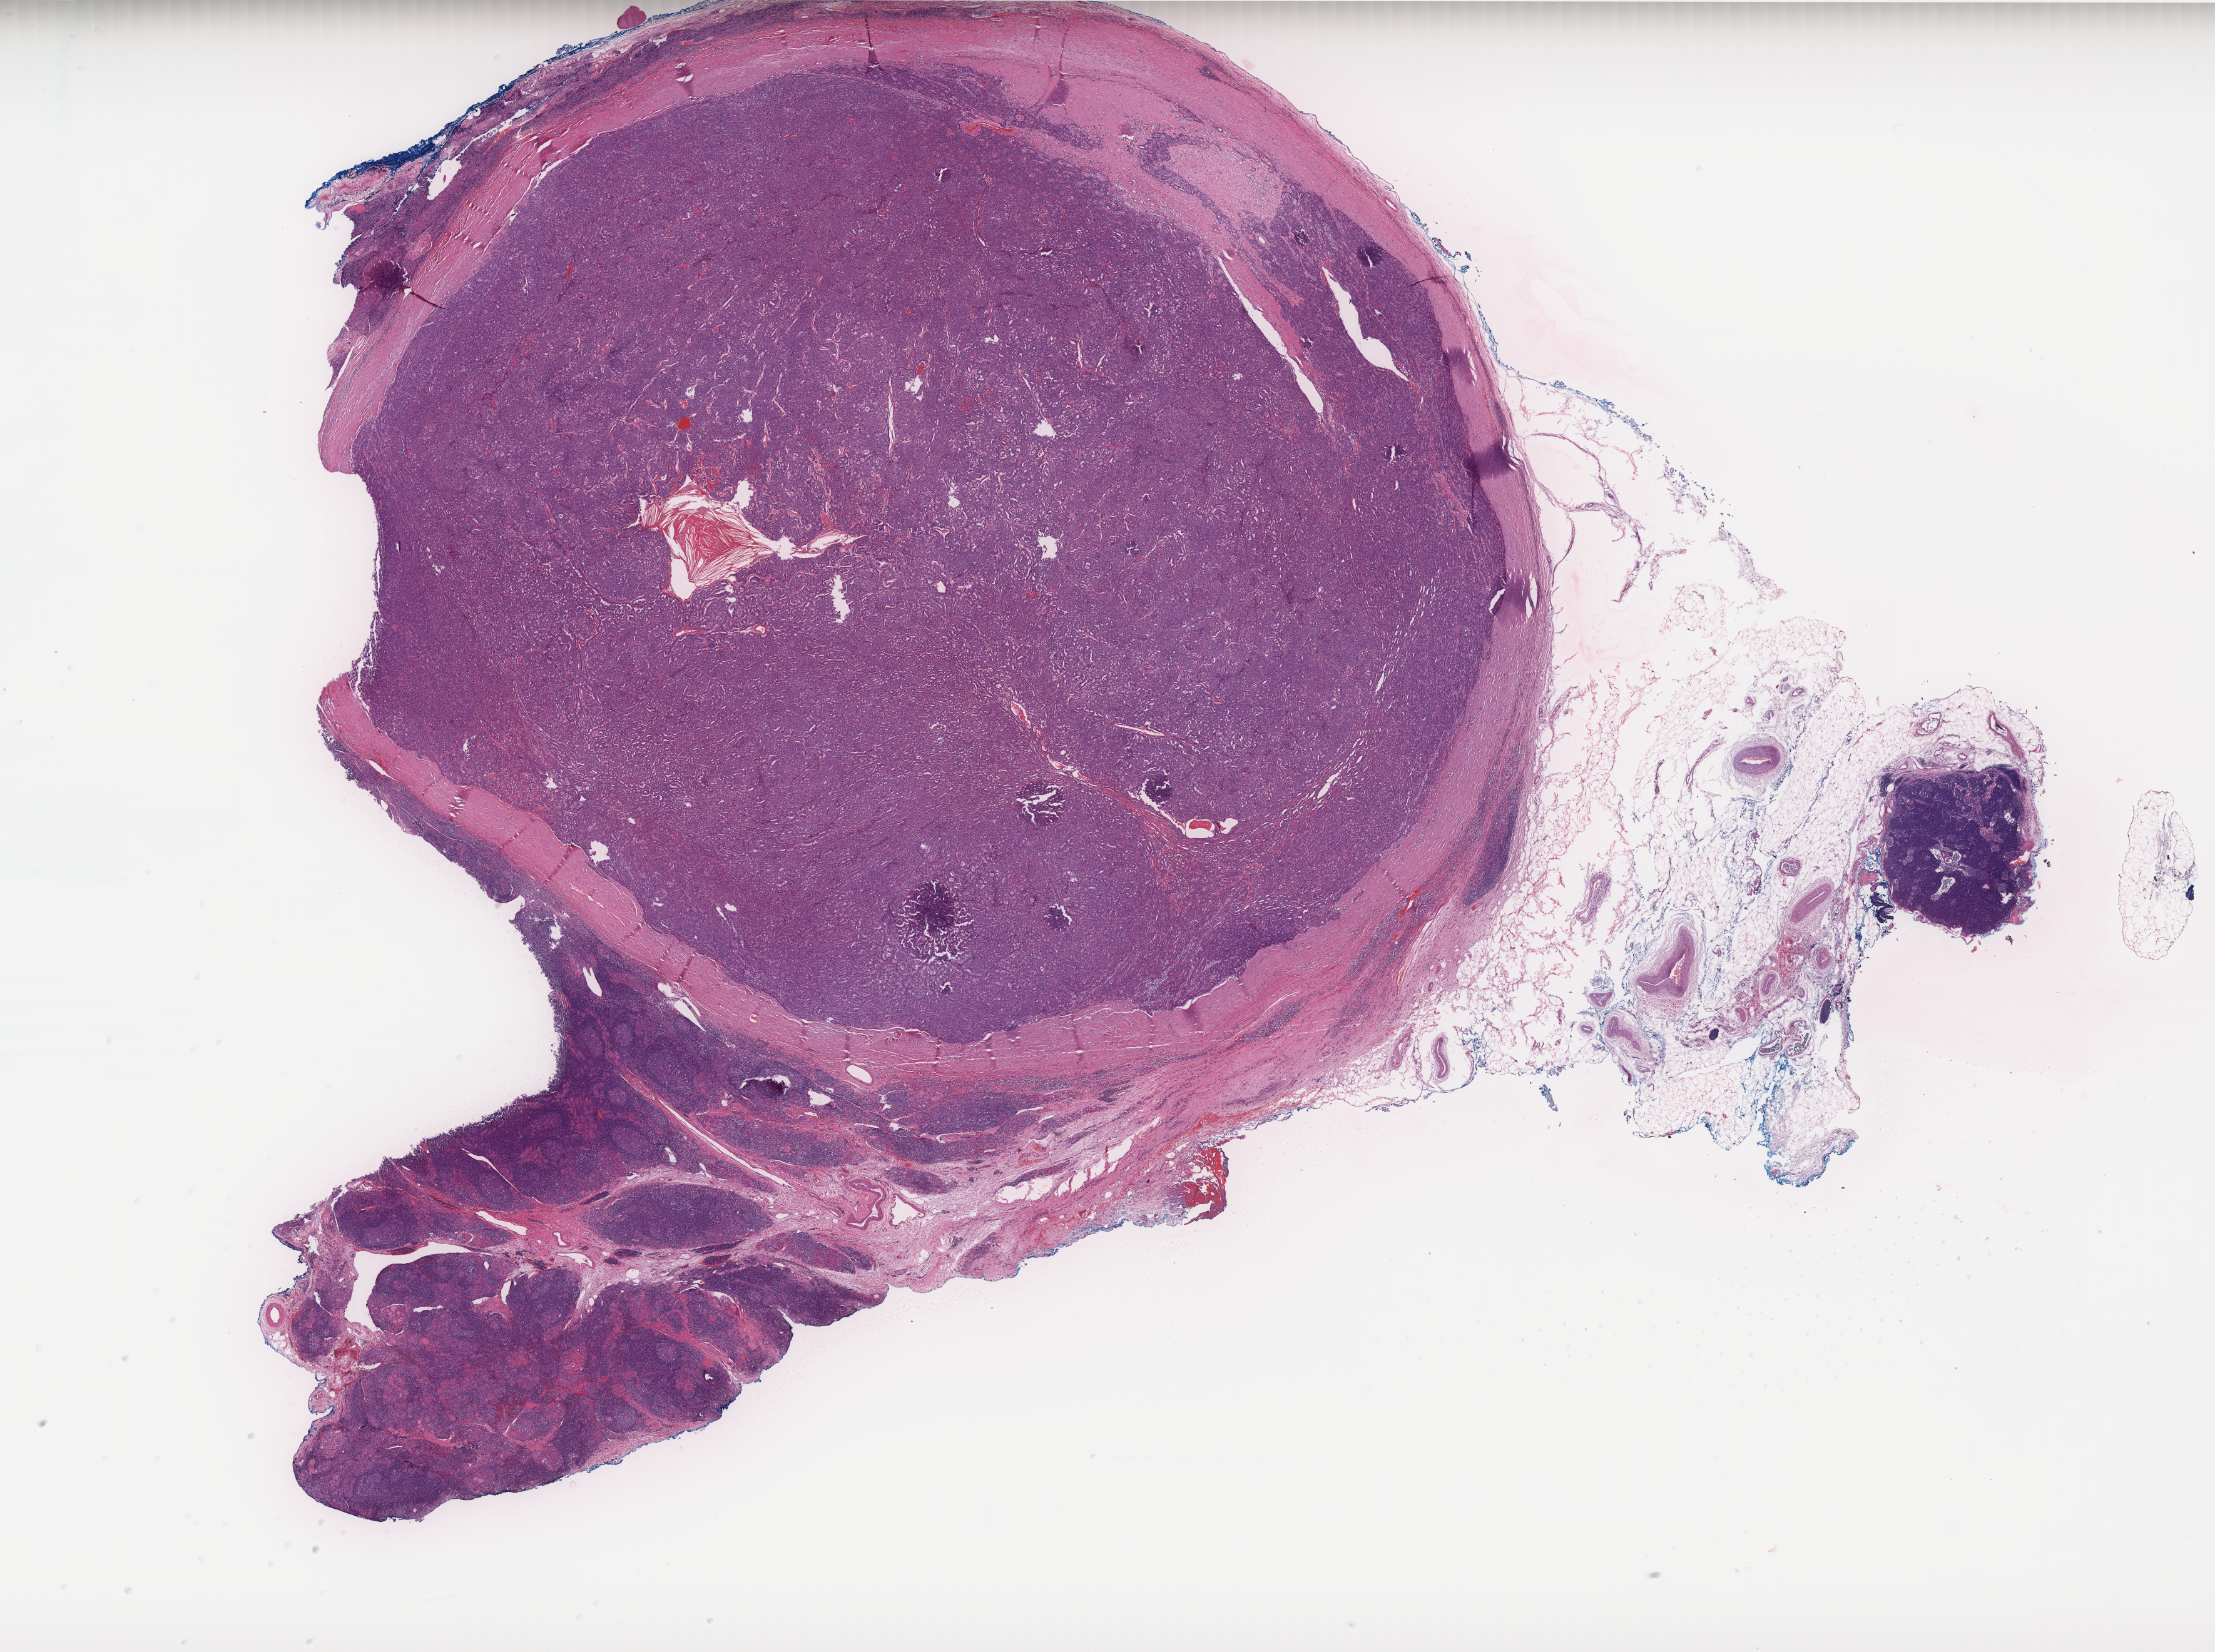
Digitized Hematoxylin and eosin (H&E) stained tissue section (whole slide), low-resolution overview of the scanned area, about 28.4 x 21.2 mm, FFPE section, sample: primary tumour, thyroid. Female patient; age at initial diagnosis 49 years.
Pathologic diagnosis: Papillary carcinoma, columnar cell. Laterality: left. AJCC pathologic stage: I (7th edition).